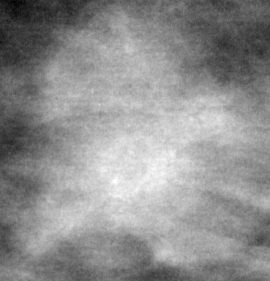
Region of interest cut from a scanned film mammogram (one marked finding), right breast, MLO view.
- Finding: mass, shape lobulated, margins ill defined; BI-RADS assessment category 4; pathology result (as recorded, not read from the image): malignant.